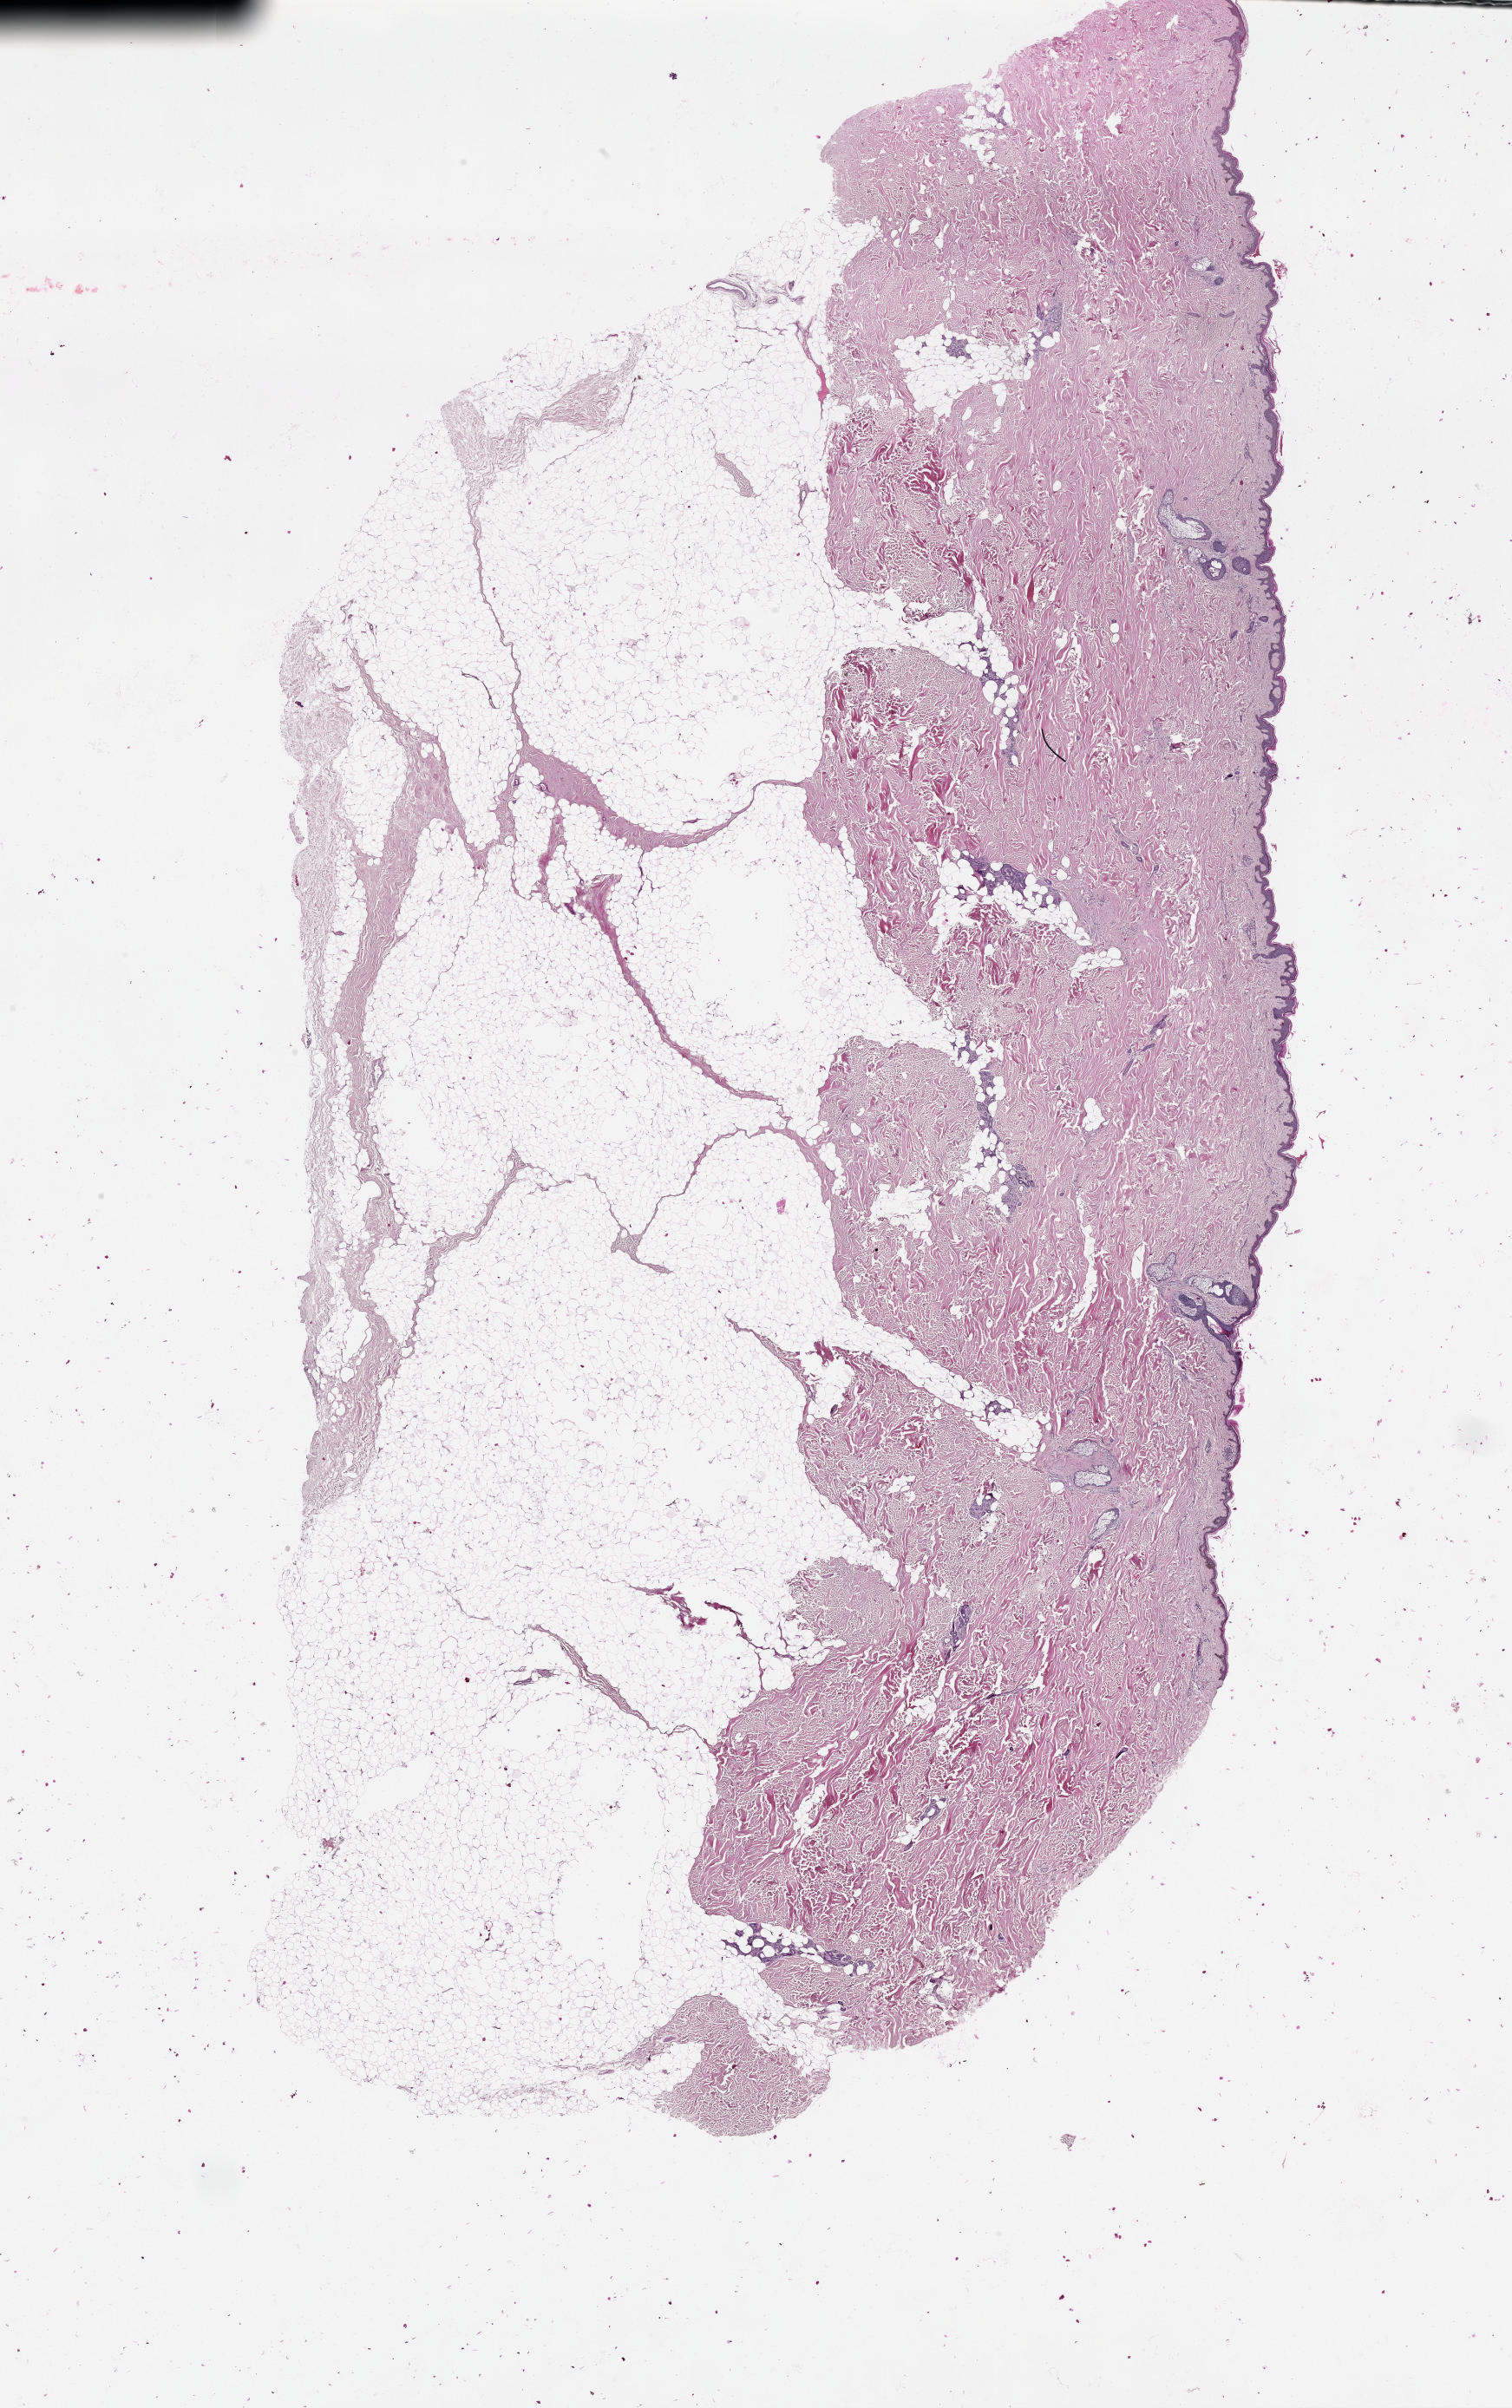
Hematoxylin and eosin (H&E) stained whole-slide image — whole scanned area (about 14.0 x 22.3 mm, acquisition: 20x scan) shown as a low-resolution overview. Patient: female, age 74 years.
Patient diagnosis: Malignant melanoma, NOS.